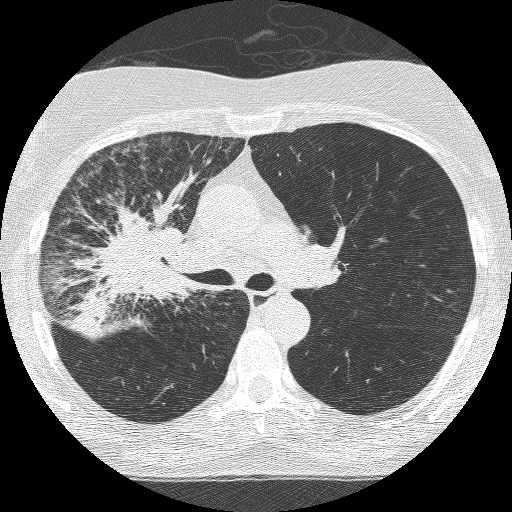
Chest CT (low-dose screening protocol), one axial image; third screening round (two years after baseline); lung window (W 1500 / L -600 HU); 1.25 mm slice thickness; slice 166 of 253 in the series; 512 × 512 image matrix. Female, age 64 years at enrolment. Former smoker at enrolment.
Expert-annotated lung lesion, box from (x=83, y=208) to (x=205, y=330) px. Reader record for this screening exam (exam-level; its link to the box is not recorded): non-calcified nodule or mass ≥4 mm, right upper lobe, 49 × 43 mm, spiculated (stellate) margins, soft tissue attenuation, pre-existing on the prior screen: yes; interval growth: yes. Official screen result: positive, other. Later outcome: lung cancer diagnosed 7 days after this screen — adenocarcinoma, NOS, right upper lobe, right middle lobe, right hilum, stage IV (AJCC 6th edition), 85 mm at pathology.